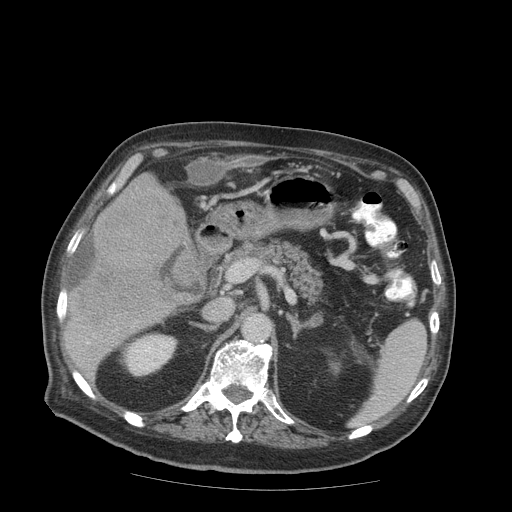
Contrast-enhanced abdominal CT (liver protocol), one axial slice; position 41 of 99 along the scan axis; reconstruction kernel STANDARD; 140 kVp; soft-tissue window (W 400 / L 40 HU); 512 × 512 image matrix, field of view 420 × 420 mm. From the clinical record (not read from this slice): diagnosis: hepatocellular carcinoma (patient treated with transarterial chemoembolisation; whether this scan precedes or follows treatment is not stated here); TNM stage (as recorded): Stage-IIIB; Child-Pugh class: A.
Outlined on this slice (semi-automatic segmentation, software-assisted and operator-edited):
- liver parenchyma outside the tumour (the mass and vessels are separate outlines, so this box may not span the whole liver): bounding box (x1, y1, x2, y2) in pixels: (66, 174, 188, 372)
- mass: (72, 192, 185, 327)
- liver vessels: (87, 342, 89, 344)